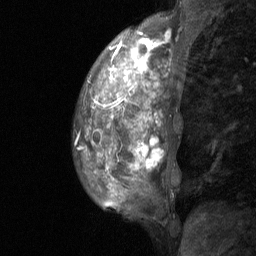
Breast MRI (dynamic contrast-enhanced), one sagittal slice. Slice 21 of 64 in the series (ordered by position). Dynamic contrast-enhanced study with each time point stored as its own series, time point 2 of 3 at this slice position (early post-contrast, ordered by acquisition time). 1.5 T. TE 4.8 ms, TR 27 ms. 2 mm slice thickness. 256 × 256 image matrix. Female patient, age 36 years. Case-level facts recorded for this patient, not image findings: setting: breast cancer imaged before/during neoadjuvant chemotherapy; receptor status: HR-positive, HER2-negative.
Structures marked on this image (semi-automatically segmented with operator editing):
- analysis volume of interest (the breast-tissue region the enhancement analysis was run in; not a lesion): bounding box <73,12,195,233> (left, top, right, bottom; pixels)
- tumour enhancement mask (voxels above the 90 % enhancement threshold inside the analysis volume of interest): <126,32,170,170>